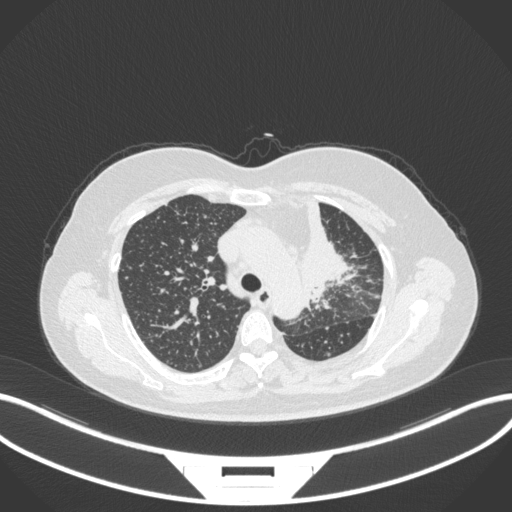
Chest CT, one axial slice. Slice 241 of 348 in the series (ordered by position). Reconstruction kernel B31f. 120 kVp. Lung window (W 1500 / L -600 HU). 512 × 512 image matrix, field of view 400 × 400 mm. Female patient, age 49 years. From the clinical record (not read from this slice): clinical TNM (as recorded): T1c N0 M1.
Annotated regions visible in this slice (bounding box drawn by a radiologist):
- lung tumour (recorded histology: adenocarcinoma): bounding box (x1, y1, x2, y2) in pixels: (291, 193, 357, 308)